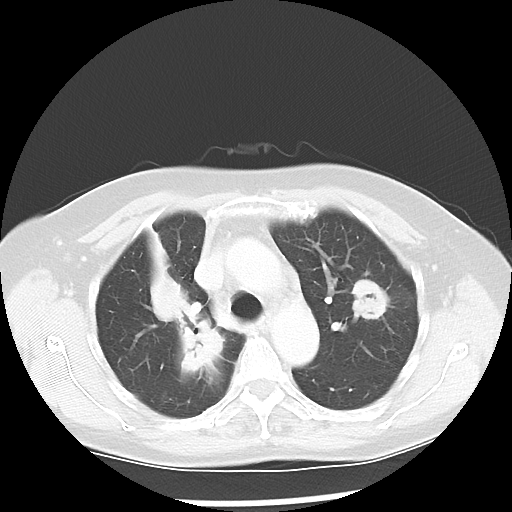
Chest CT, one axial slice. Slice 36 of 52 in the series (ordered by position). Lung window (W 1500 / L -600 HU). 512 × 512 image matrix, field of view 328 × 328 mm. Patient: female, 60 years. From the clinical record (not read from this slice): clinical TNM (as recorded): T2 N1 M1a.
Structures marked on this image (rectangle marked by the reading radiologist):
- lung tumour (recorded histology: adenocarcinoma): bounding box [x1, y1, x2, y2] px = [146, 265, 230, 386]